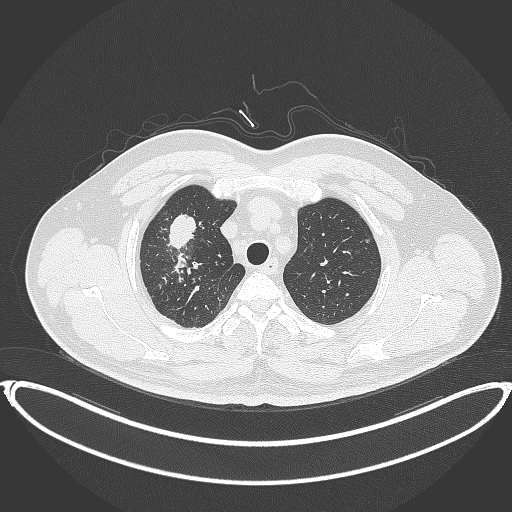
Chest CT, one axial slice; position 316 of 399 along the scan axis; lung window (W 1500 / L -600 HU); 1 mm slice thickness; 512 × 512 image matrix. Patient: male, 53 years. From the clinical record (not read from this slice): clinical TNM (as recorded): T2a N0 M0.
Annotated regions visible in this slice (bounding box drawn by a radiologist):
- lung tumour (recorded histology: adenocarcinoma): bounding box (x1, y1, x2, y2) in pixels: (165, 211, 204, 250)